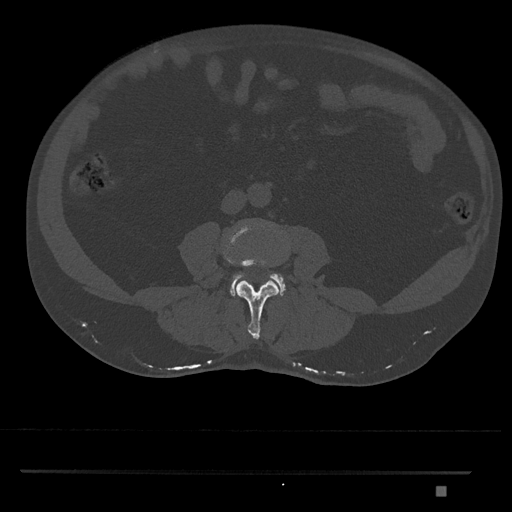
CT including the spine, one axial slice. Position 658 of 1134 along the scan axis. Reconstruction kernel Br40s/3. 120 kVp. Bone window (W 1800 / L 400 HU). 0.5 mm slice thickness. 512 × 512 image matrix. Patient: male, 65 years. From the clinical record (not read from this slice): primary cancer: prostate.
Outlined on this slice (semi-automatically segmented with operator editing):
- L3 vertebra: bounding box <222,221,280,339> (left, top, right, bottom; pixels)
- L4 vertebra: <229,272,286,297>